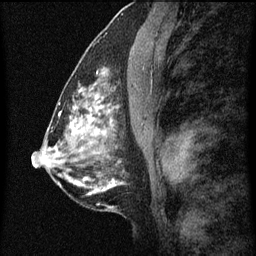
Breast MRI (dynamic contrast-enhanced), one sagittal slice; slice 31 of 60 in the series (ordered by position); dynamic contrast-enhanced series, image 2 of 7 at this slice position (ordered by acquisition); 1.5 T; TE 4.2 ms, TR 8 ms; 2 mm slice thickness; 256 × 256 image matrix. Female patient, age 51 years.
Annotated regions visible in this slice (semi-automatic segmentation, software-assisted and operator-edited):
- analysis volume of interest (the breast-tissue region the enhancement analysis was run in; not a lesion): bounding box [x1, y1, x2, y2] px = [86, 48, 116, 101]
- tumour enhancement mask (voxels above the 70 % enhancement threshold inside the analysis volume of interest): [90, 70, 107, 101]